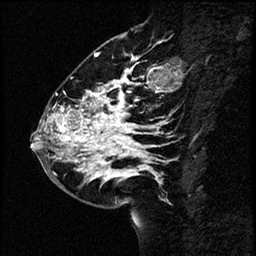
Breast MRI (dynamic contrast-enhanced), one sagittal slice. Slice 26 of 60 in the series (ordered by position). Dynamic contrast-enhanced study with each time point stored as its own series, time point 2 of 4 at this slice position (early post-contrast, ordered by acquisition time). 1.5 T. TE 4.2 ms, TR 17.6 ms. 256 × 256 image matrix, field of view 200 × 200 mm. Female patient, age 43 years. Case-level facts recorded for this patient, not image findings: setting: breast cancer imaged before/during neoadjuvant chemotherapy.
Structures marked on this image (semi-automatic segmentation, software-assisted and operator-edited):
- analysis volume of interest (the breast-tissue region the enhancement analysis was run in; not a lesion): bounding box (x1, y1, x2, y2) in pixels: (34, 56, 169, 191)
- tumour enhancement mask (voxels above the 100 % enhancement threshold inside the analysis volume of interest): (35, 56, 163, 179)